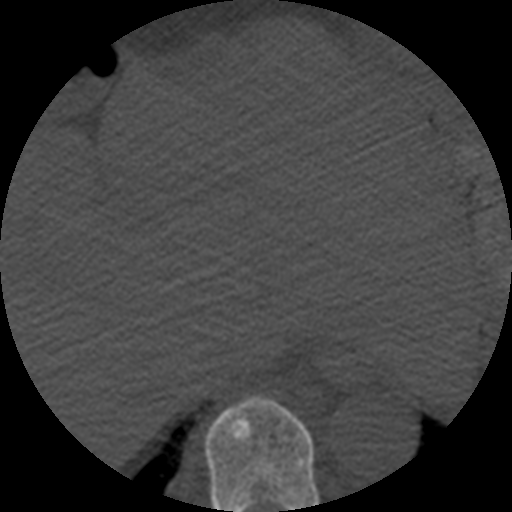
CT including the spine, one axial slice; slice 288 of 508 in the series (ordered by position); reconstruction kernel STANDARD; 120 kVp; bone window (W 1800 / L 400 HU); 512 × 512 image matrix, field of view 160 × 160 mm. Patient age 57 years. Case-level facts recorded for this patient, not image findings: primary cancer: prostate.
Outlined on this slice (semi-automatically segmented with operator editing):
- T9 vertebra: box from (x=205, y=397) to (x=320, y=512) px